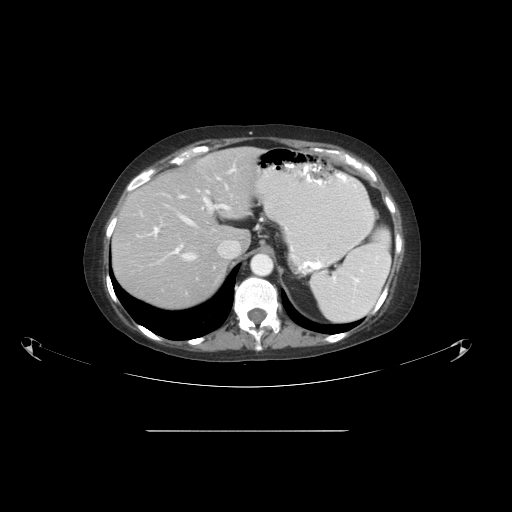
Contrast-enhanced abdominal CT, one axial slice; position 38 of 51 along the scan axis; reconstruction kernel STANDARD; 120 kVp; intravenous contrast given; soft-tissue window (W 400 / L 40 HU); 5 mm slice thickness; 512 × 512 image matrix. Female patient, age 48 years. From the clinical record (not read from this slice): diagnosis: colorectal cancer liver metastases, imaged before liver resection; multiple liver metastases: yes; largest metastasis: 1 cm.
Annotated regions visible in this slice (manually delineated by an expert):
- hepatic veins: bounding box (x1, y1, x2, y2) in pixels: (145, 185, 240, 267)
- liver: (114, 148, 261, 309)
- planned liver remnant (the part of the liver to remain after resection): (114, 170, 230, 310)
- portal vein (with intrahepatic branches): (148, 165, 236, 254)
- liver metastasis: (204, 163, 208, 168)